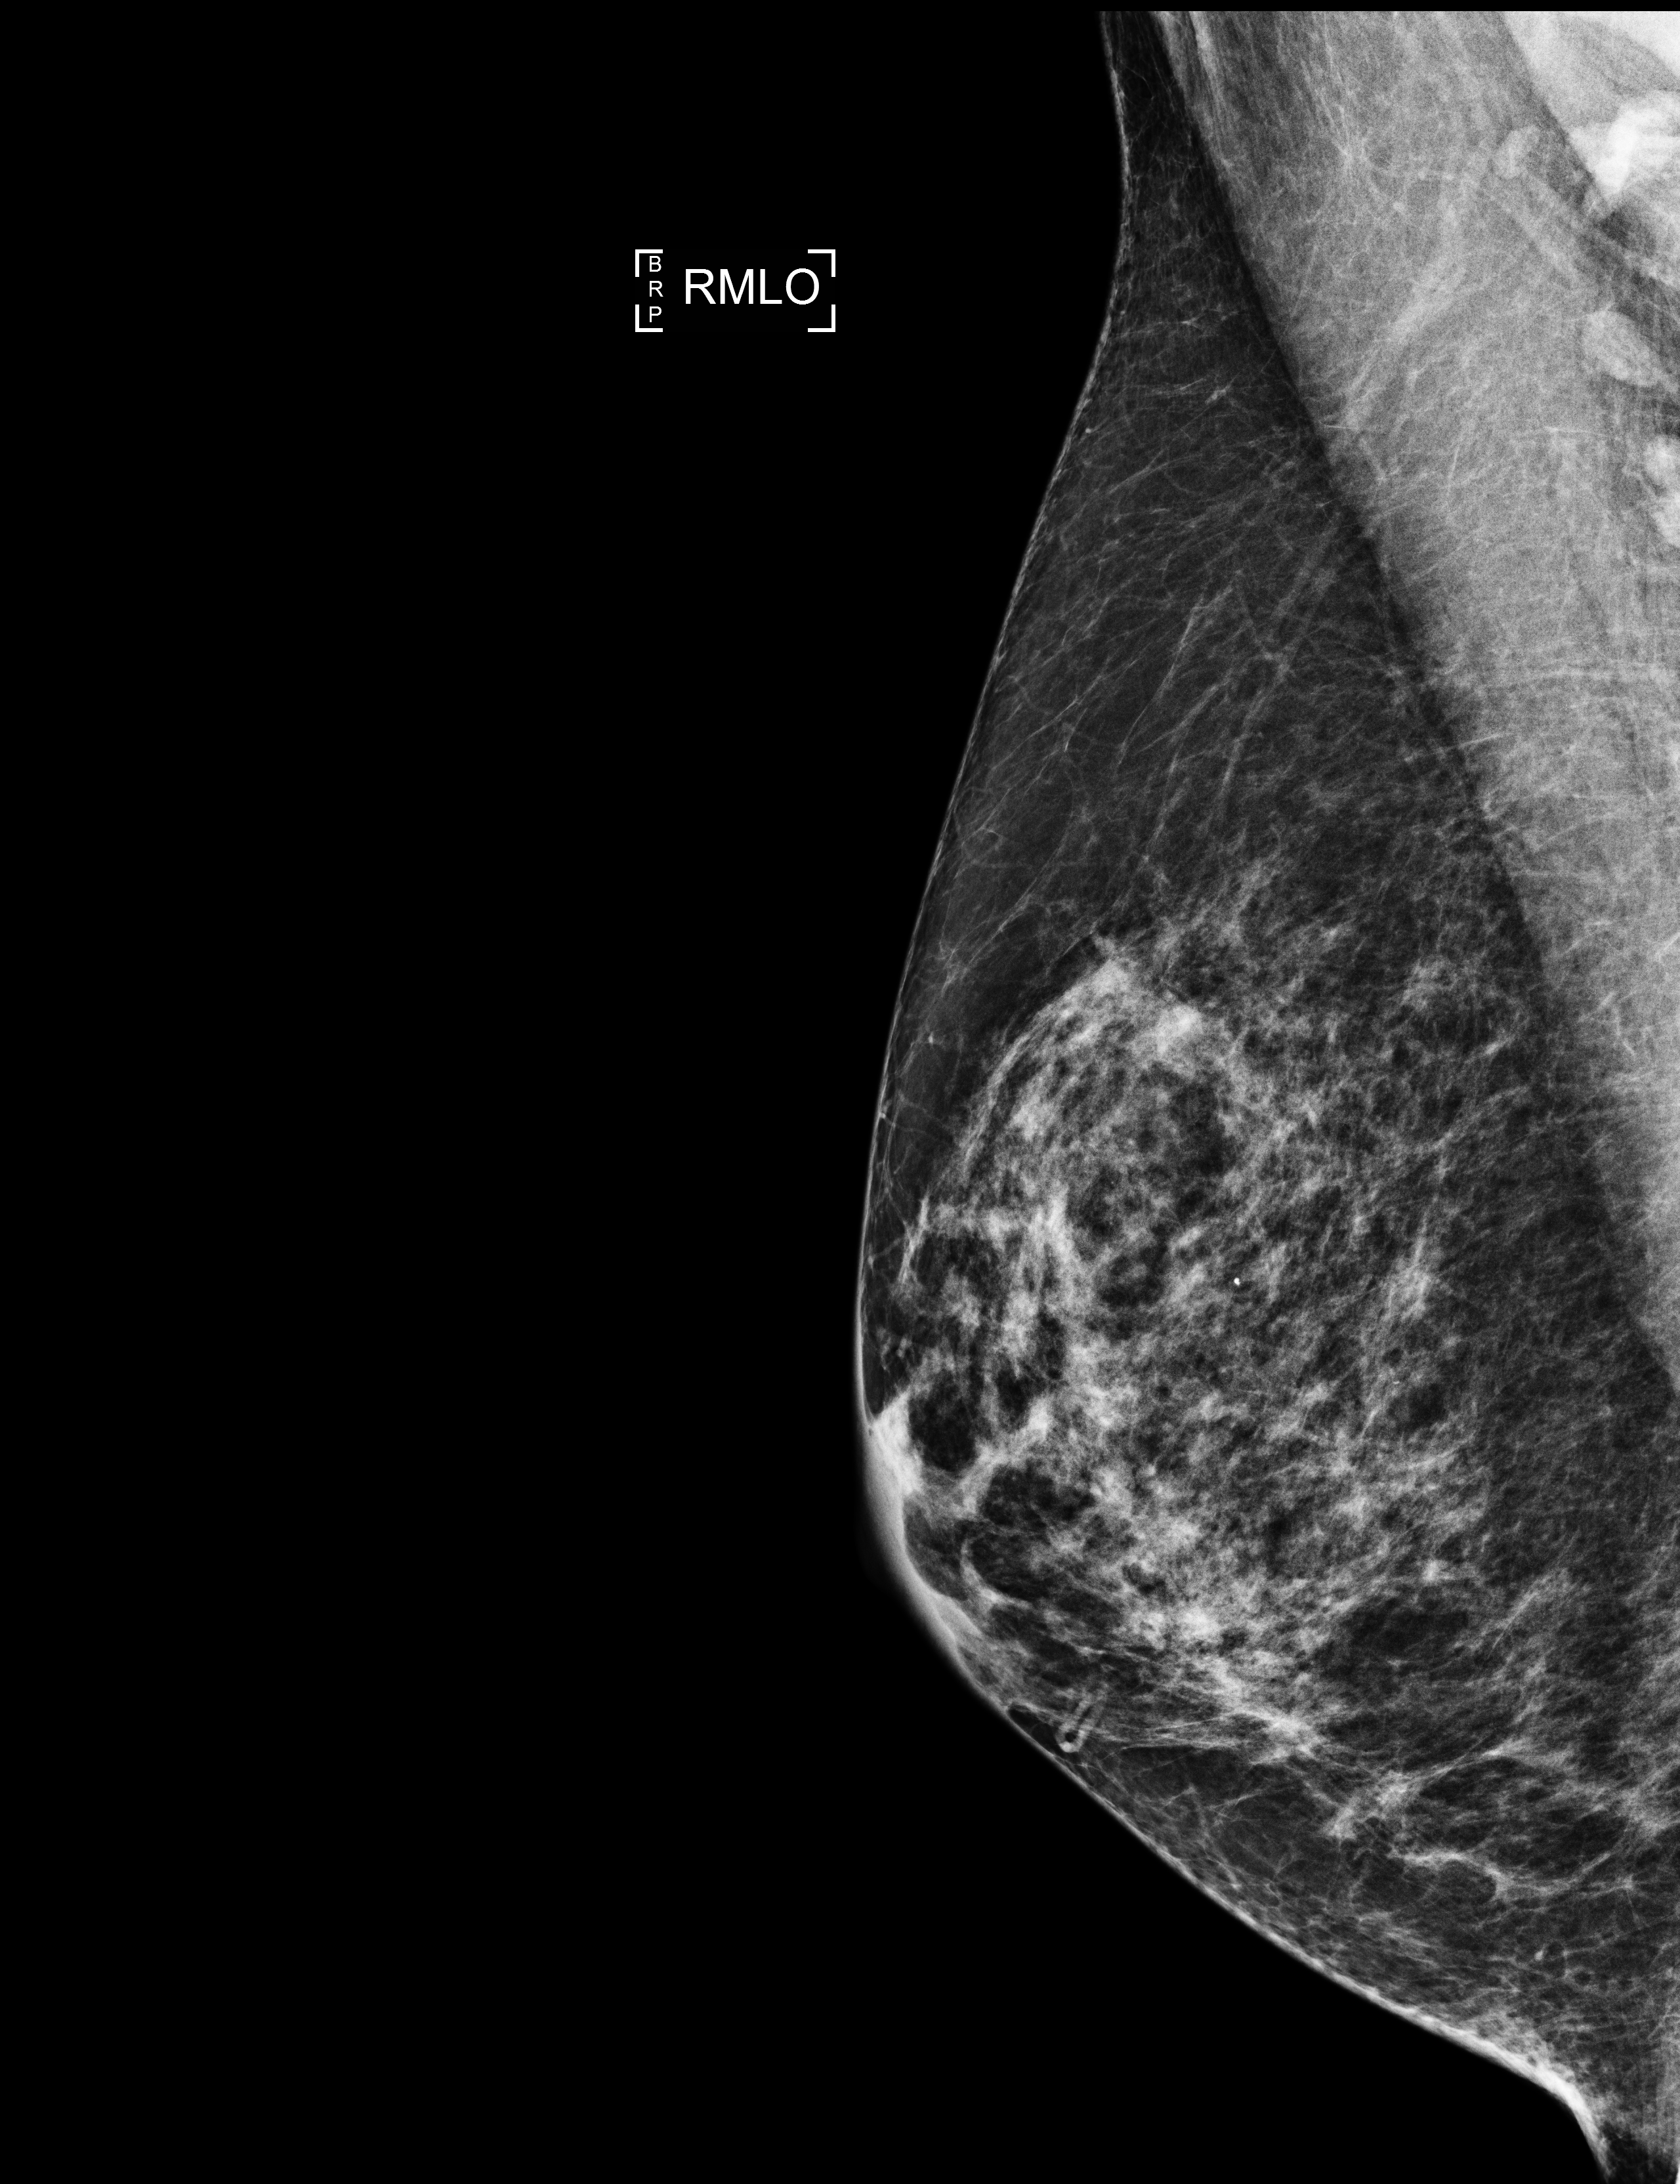
Digital mammogram (FFDM); right breast; medio-lateral oblique projection; annual screening mammography examination; compressed breast thickness 56 mm. Female patient, age 63 years.
BI-RADS breast density category at the screening exam (both breasts, scale 1–4): 3. Final BI-RADS category for the screening round (tomosynthesis exam, both breasts): category 2. Recall: no recall after this screen.